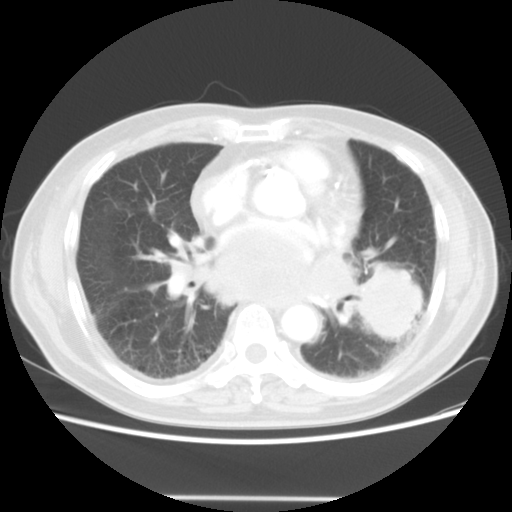
Chest CT, one axial slice. Position 23 of 56 along the scan axis. 140 kVp. Lung window (W 1500 / L -600 HU). 5 mm slice thickness. 512 × 512 image matrix. Patient: male, 66 years. From the clinical record (not read from this slice): clinical TNM (as recorded): T4 N3 M0; histopathological grade: G3.
Structures marked on this image (rectangle marked by the reading radiologist):
- lung tumour (recorded histology: small cell carcinoma): box from (x=362, y=255) to (x=425, y=346) px